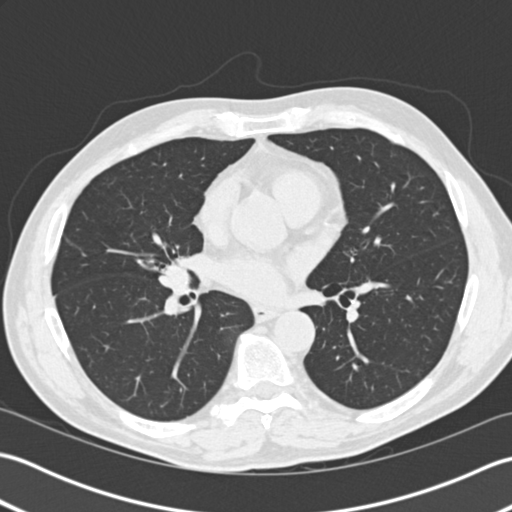
Axial slice from a low-dose chest CT screening exam. Second screening round (one year after baseline). Lung window (W 1500 / L -600 HU). 2 mm slice thickness. Standard (soft-tissue) reconstruction kernel (B30f). 140 kVp. Slice 100 of 192 in the series. Male, age 57 years at enrolment. Former smoker at enrolment.
Lesion marked by an expert reader, bounding box <155,252,196,293> (left, top, right, bottom; pixels). Screening reader's record for this exam: no non-calcified nodule ≥4 mm recorded. Official screen result: negative screen, significant abnormalities not suspicious for lung cancer. Participant outcome: lung cancer diagnosed 483 days after this screen — carcinoid tumor, NOS, right middle lobe, carcinoid, stage not assessed, 15 mm at pathology.